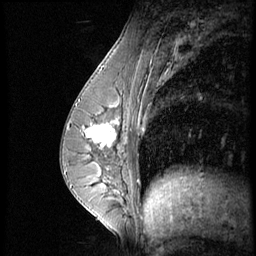
Breast MRI (dynamic contrast-enhanced), one sagittal slice; slice 26 of 56 in the series (ordered by position); dynamic contrast-enhanced series, image 2 of 4 at this slice position (ordered by acquisition); 1.5 T; TE 4.2 ms, TR 8.9 ms; 256 × 256 image matrix, field of view 200 × 200 mm. Patient: female, 35 years. From the clinical record (not read from this slice): setting: breast cancer imaged before/during neoadjuvant chemotherapy; receptor status: HER2-positive.
Outlined on this slice (semi-automatic segmentation, software-assisted and operator-edited):
- analysis volume of interest (the breast-tissue region the enhancement analysis was run in; not a lesion): bounding box (x1, y1, x2, y2) in pixels: (73, 111, 131, 164)
- tumour enhancement mask (voxels above the 140 % enhancement threshold inside the analysis volume of interest): (79, 117, 118, 164)